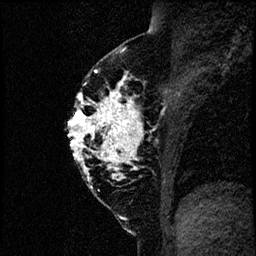
Breast MRI (dynamic contrast-enhanced), one sagittal slice. Position 39 of 60 along the scan axis. Dynamic contrast-enhanced study with each time point stored as its own series, time point 2 of 4 at this slice position (early post-contrast, ordered by acquisition time). 1.5 T. TE 4.2 ms, TR 17.6 ms. 2 mm slice thickness. 256 × 256 image matrix. Female patient, age 40 years. Case-level facts recorded for this patient, not image findings: setting: breast cancer imaged before/during neoadjuvant chemotherapy; receptor status: HER2-positive.
Annotated regions visible in this slice (semi-automatic segmentation, software-assisted and operator-edited):
- analysis volume of interest (the breast-tissue region the enhancement analysis was run in; not a lesion): box from (x=66, y=55) to (x=185, y=206) px
- tumour enhancement mask (voxels above the 100 % enhancement threshold inside the analysis volume of interest): (x=67, y=70)–(x=139, y=180)